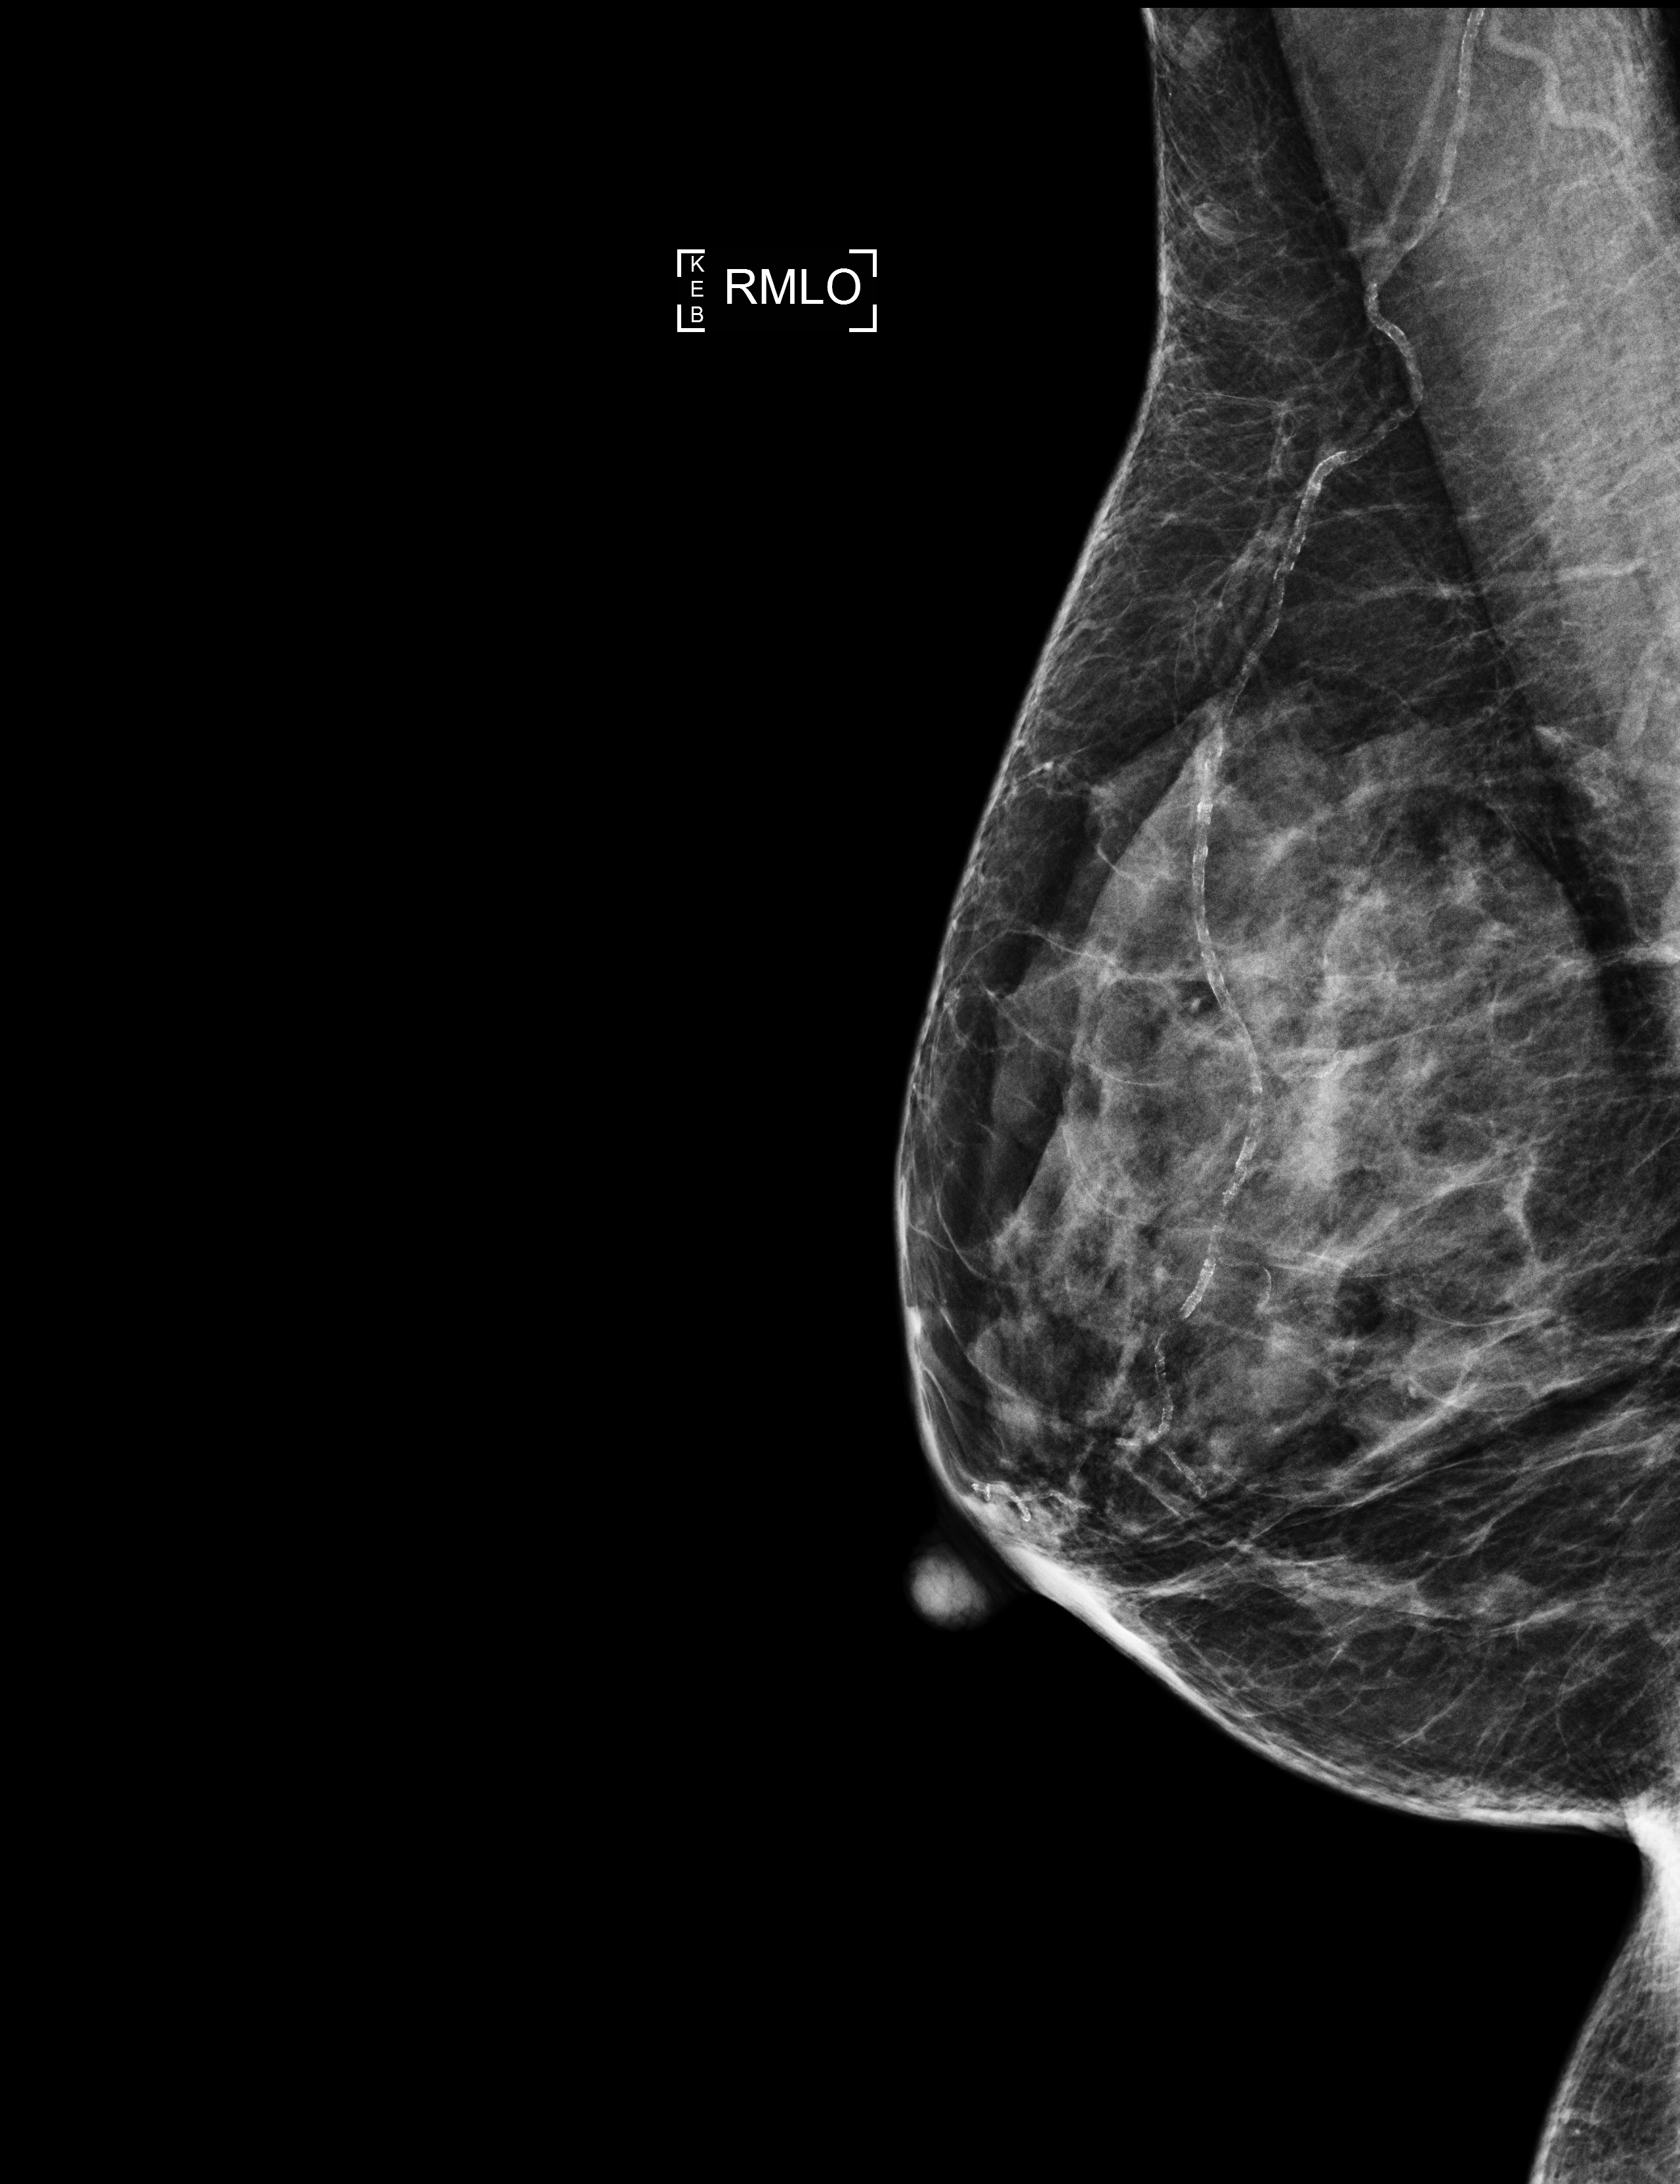
Annual screening mammography examination, compressed breast thickness 39 mm, system: Selenia Dimensions. Female patient, age 76 years.
Image type: full-field digital mammogram. Breast: right. Projection: MLO view.